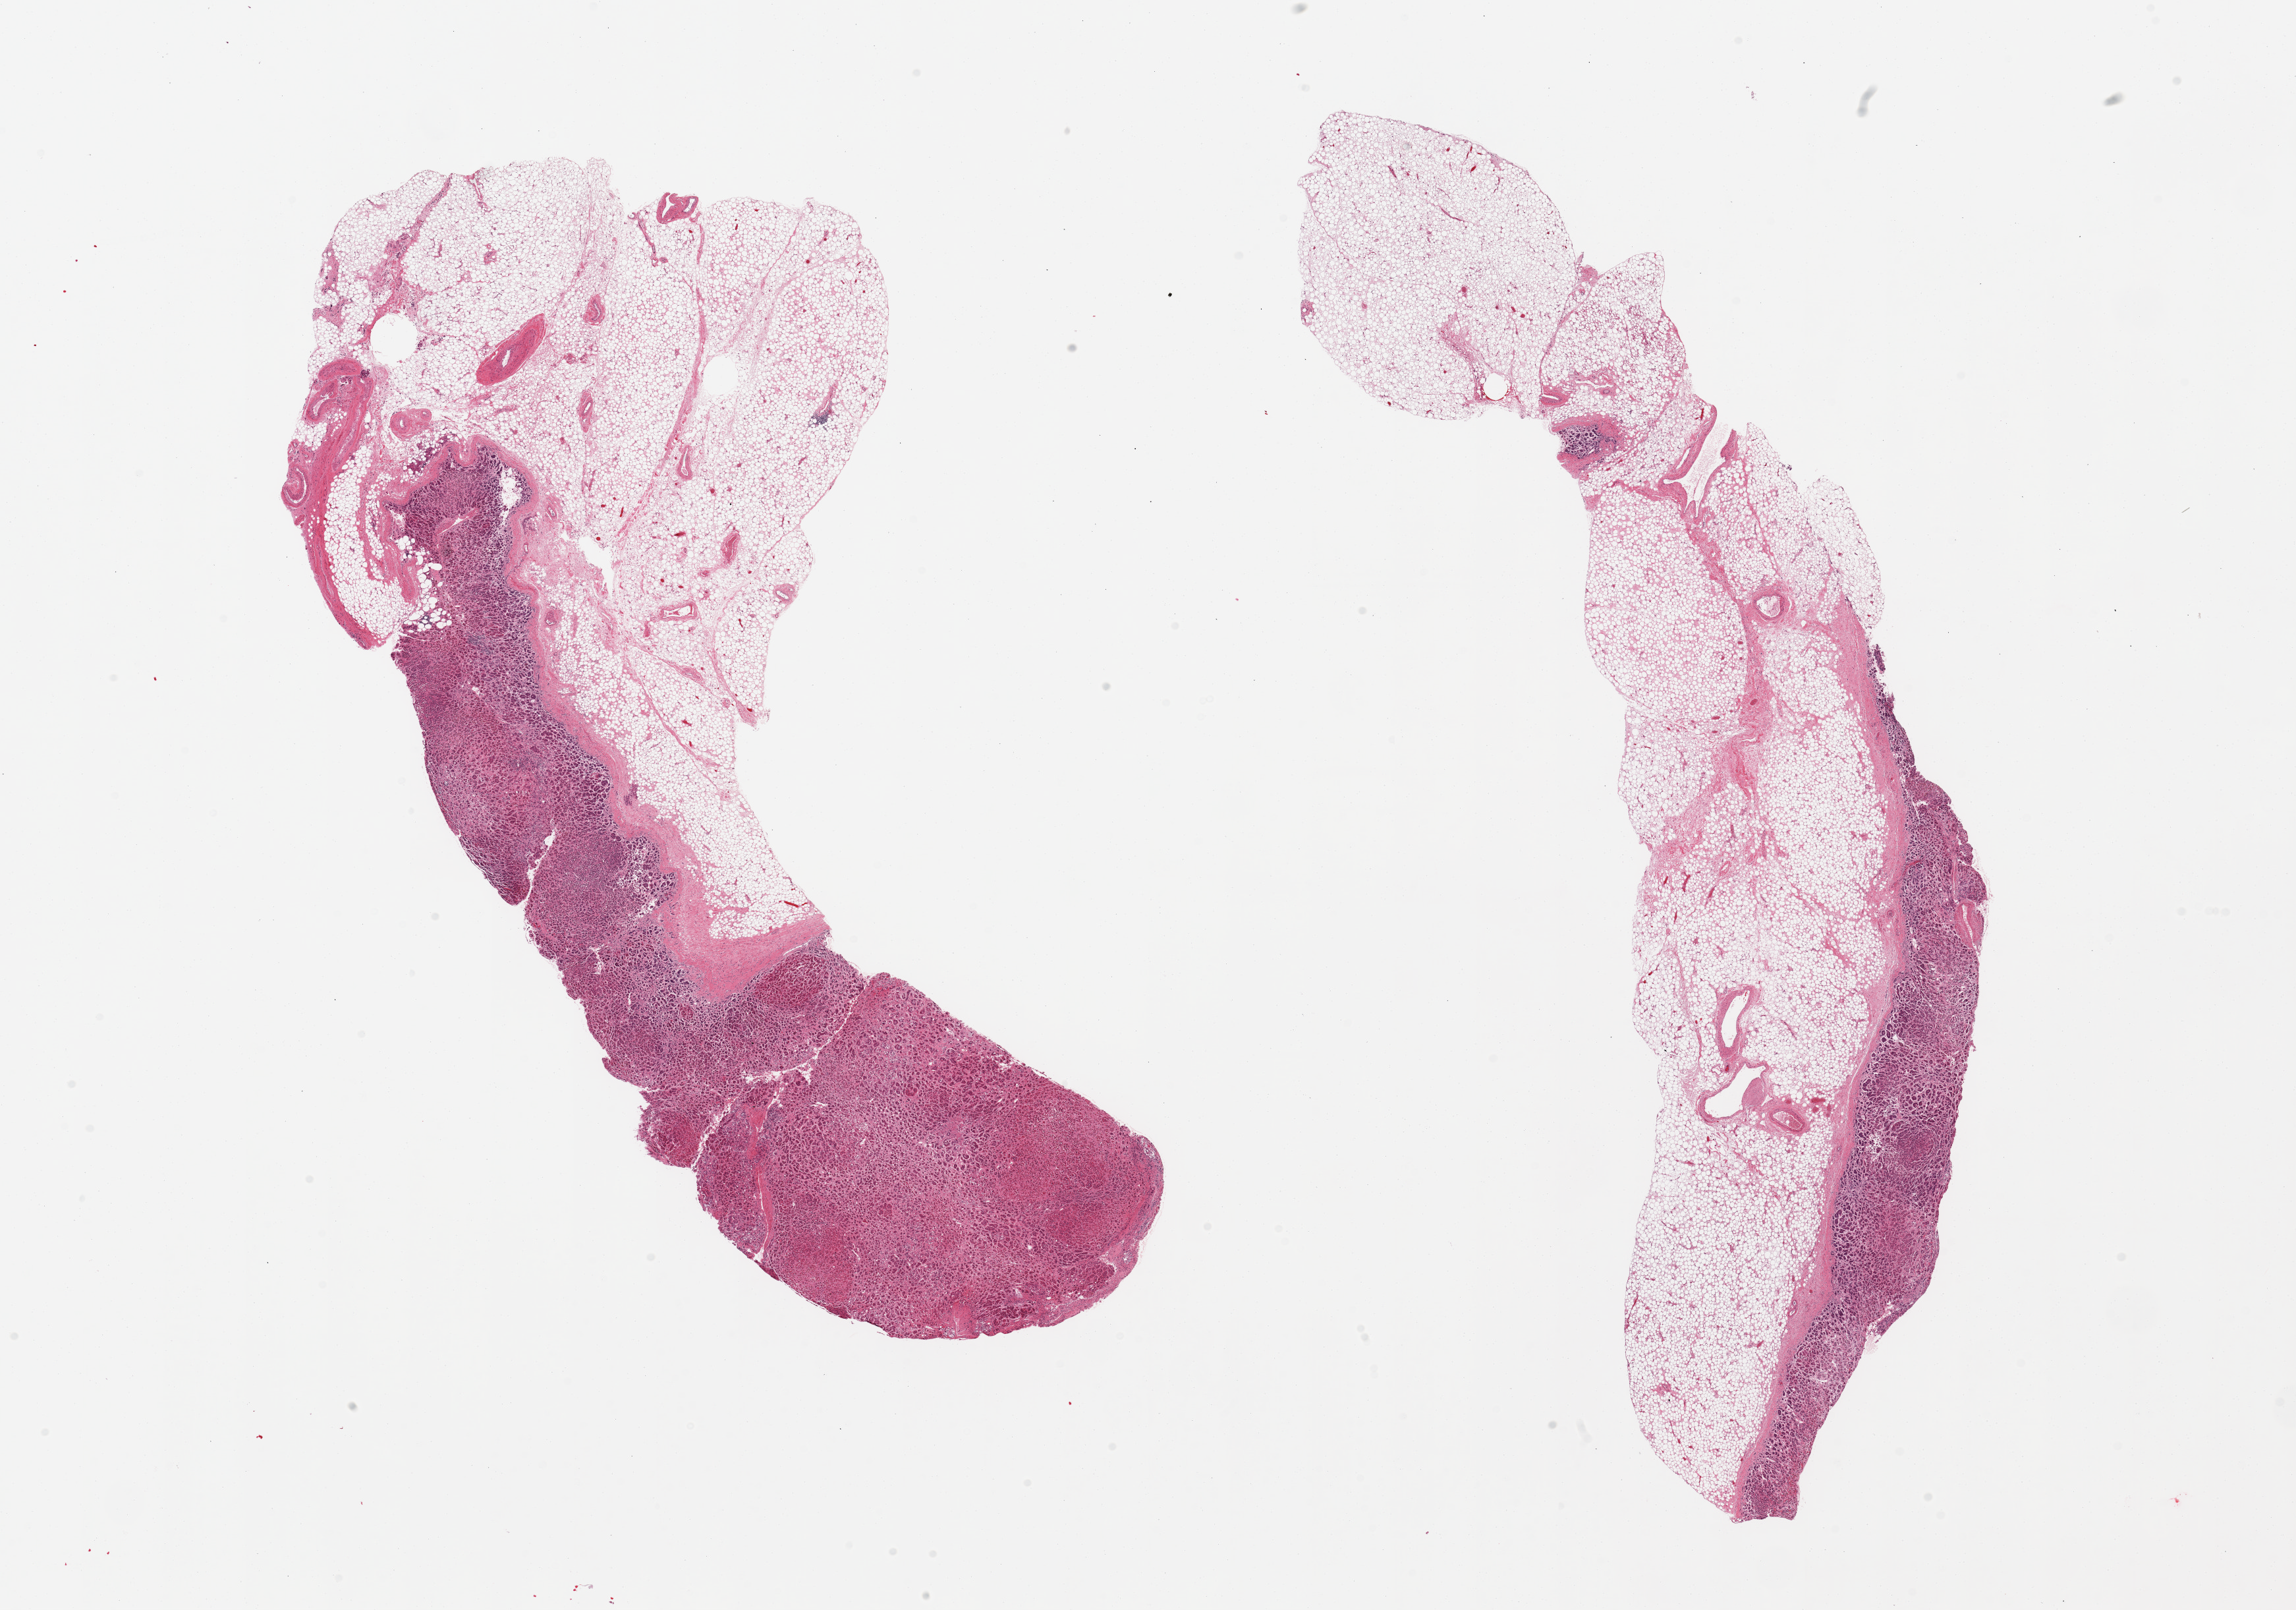
H&E whole-slide image, brightfield, whole scanned area (about 27.6 x 19.3 mm) shown as a low-resolution overview, PAXgene-fixed, paraffin-embedded tissue, section of adrenal gland (target tissue), tissue donor sample. Male donor.
Review note (as recorded): 2 pieces, cortex, ~50% of specimen; rest is adherent fat.